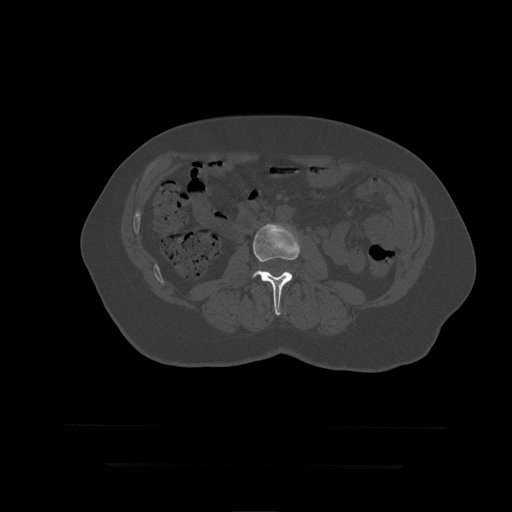
CT including the spine, one axial slice. Position 120 of 399 along the scan axis. Reconstruction kernel STANDARD. Bone window (W 1800 / L 400 HU). 1.25 mm slice thickness. 512 × 512 image matrix. Patient age 41 years. From the clinical record (not read from this slice): primary cancer: breast.
Outlined on this slice (semi-automatic segmentation, software-assisted and operator-edited):
- L3 vertebra: bounding box [x1, y1, x2, y2] px = [252, 224, 301, 316]